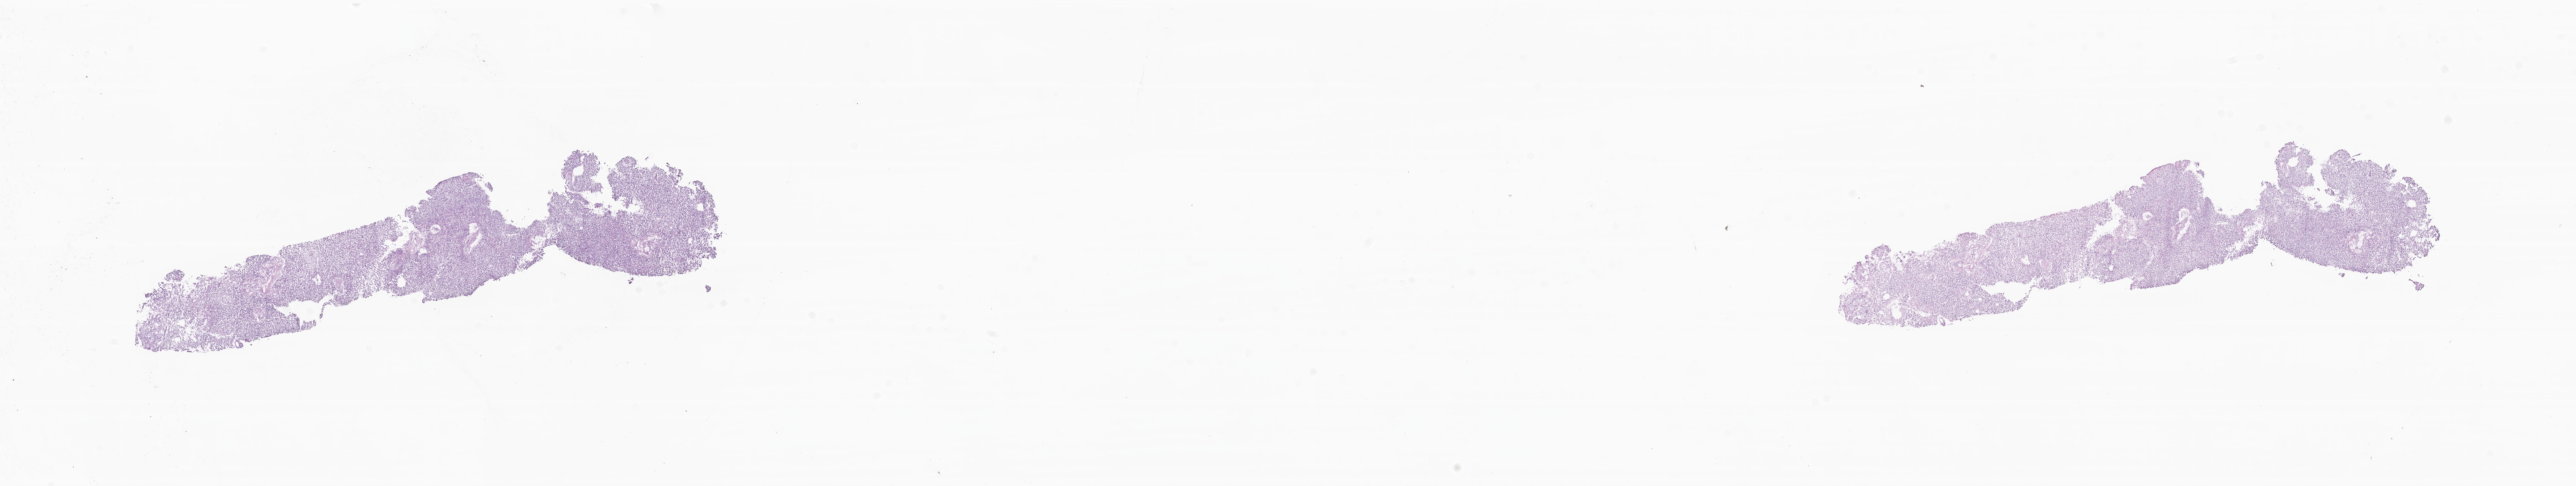
Hematoxylin and eosin (H&E) whole-slide image of tumor tissue from the brain — low-resolution overview of the scanned area, about 34.7 x 6.6 mm. Frozen section. Patient: male, age 124 months.
Recorded diagnosis: Neoplasm, uncertain whether benign or malignant.